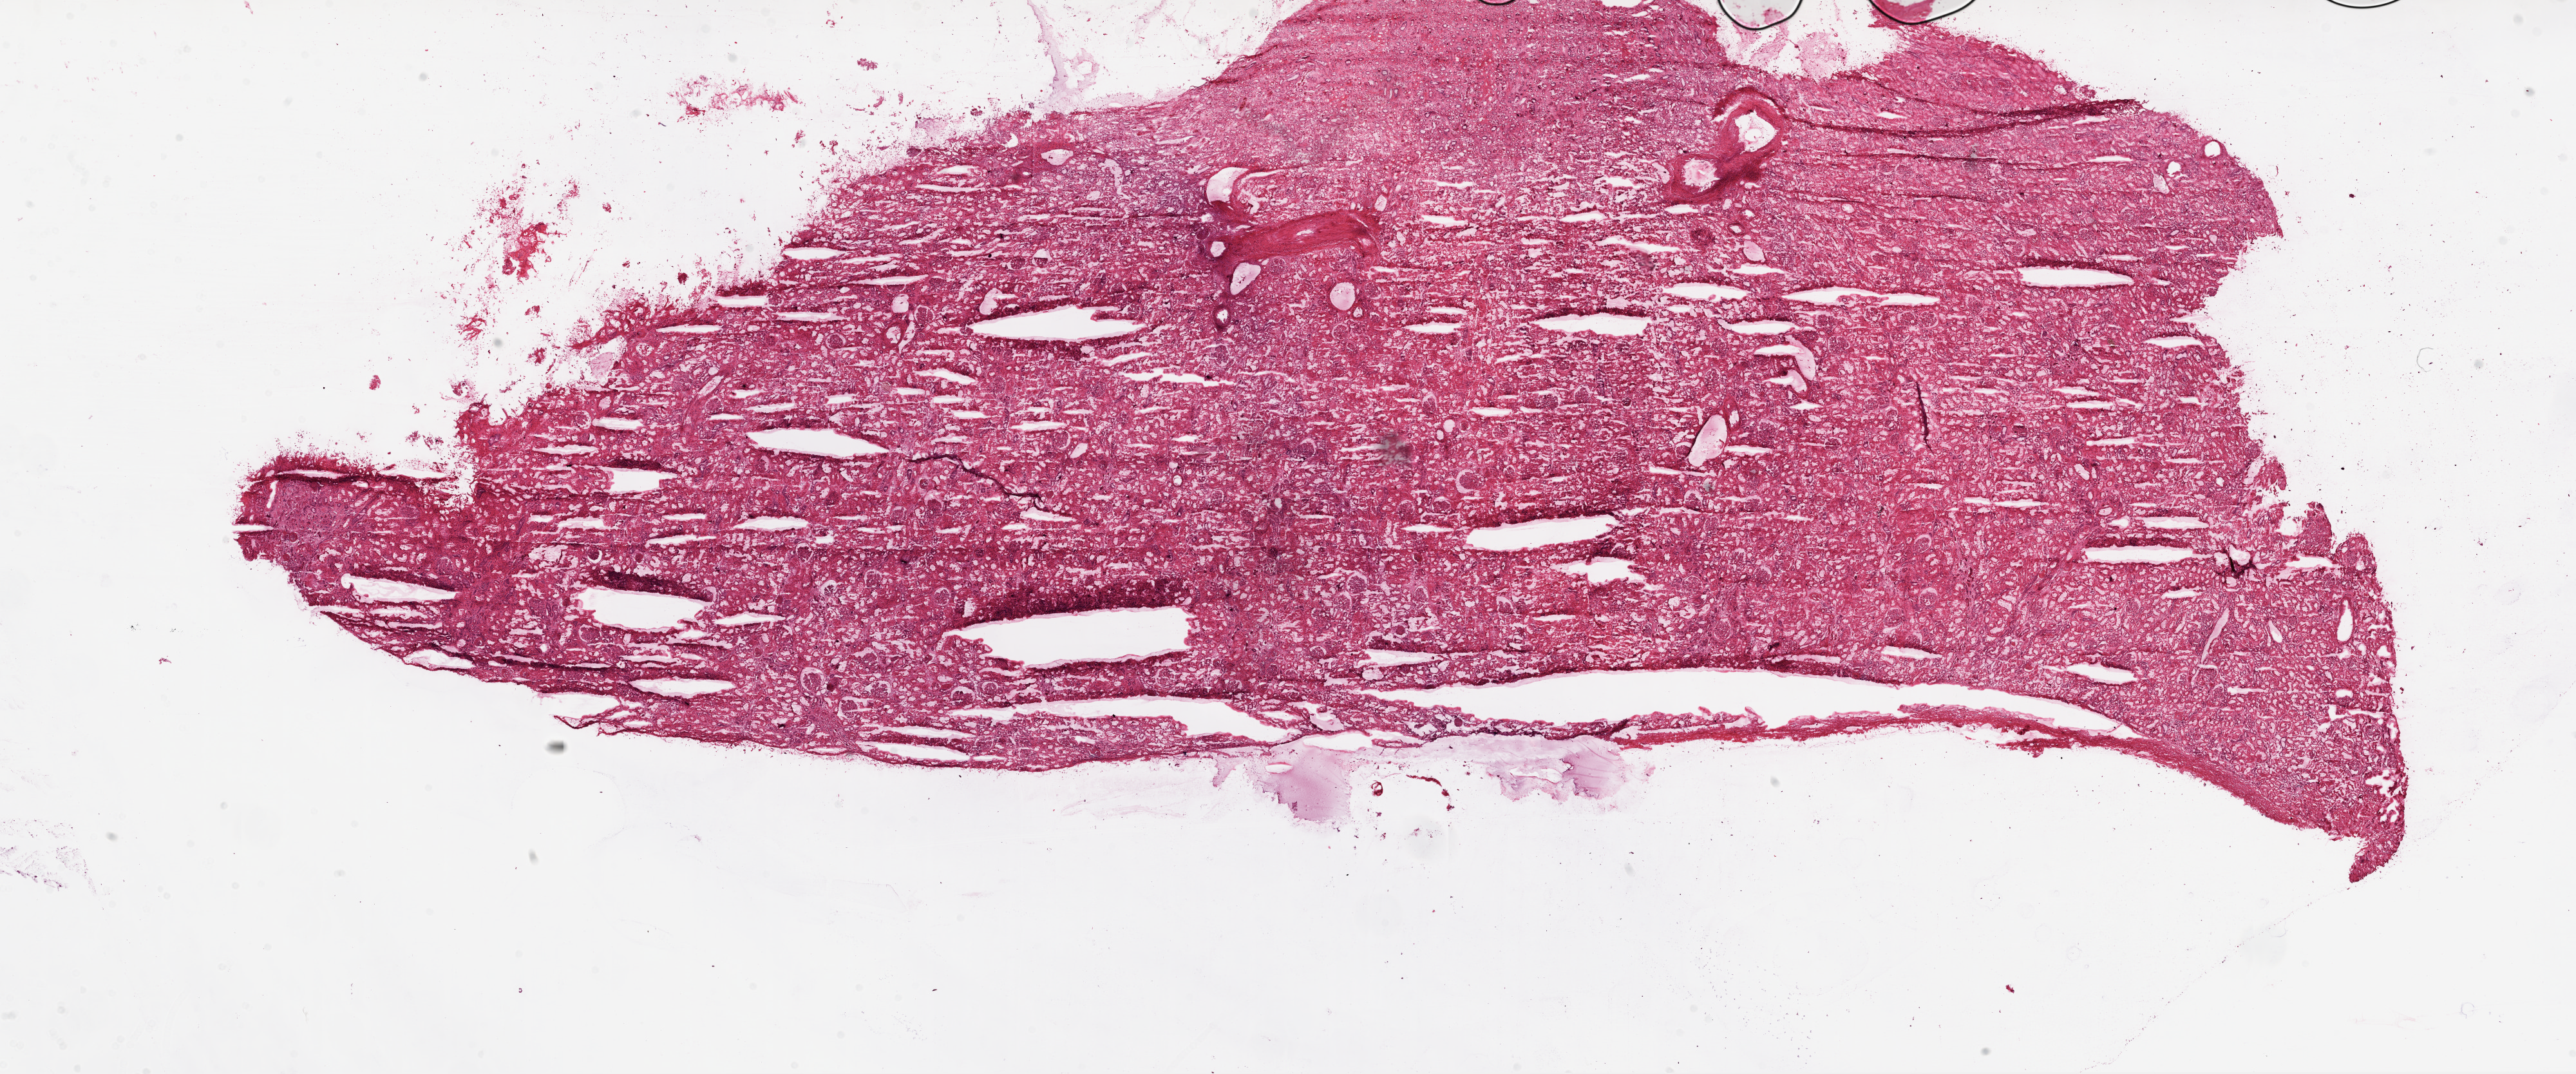
Whole-slide histology image, Hematoxylin and eosin (H&E) stained, a low-resolution overview of the entire scanned area, about 32.1 x 13.4 mm (slide scanned at 20x); frozen section from the top of the tissue portion; kidney, solid tissue normal (non-tumour tissue) sample. Patient: female, age at initial diagnosis 61 years.
* this section: solid tissue normal sample (biorepository sample class)
* patient diagnosis: Clear cell adenocarcinoma, NOS